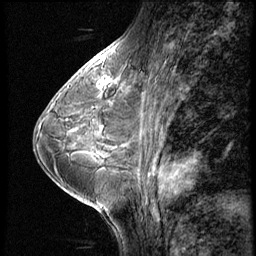
Breast MRI (dynamic contrast-enhanced), one sagittal slice; slice 26 of 56 in the series (ordered by position); 4 images stored at this slice position (order not interpretable as contrast timing); 1.5 T; TE 4.2 ms, TR 8.9 ms; 256 × 256 image matrix. Female patient, age 38 years. Case-level facts recorded for this patient, not image findings: setting: breast cancer imaged before/during neoadjuvant chemotherapy; receptor status: triple-negative.
Structures marked on this image (semi-automatic segmentation, software-assisted and operator-edited):
- analysis volume of interest (the breast-tissue region the enhancement analysis was run in; not a lesion): bounding box [x1, y1, x2, y2] px = [88, 73, 115, 102]
- tumour enhancement mask (voxels above the 140 % enhancement threshold inside the analysis volume of interest): [97, 80, 113, 89]